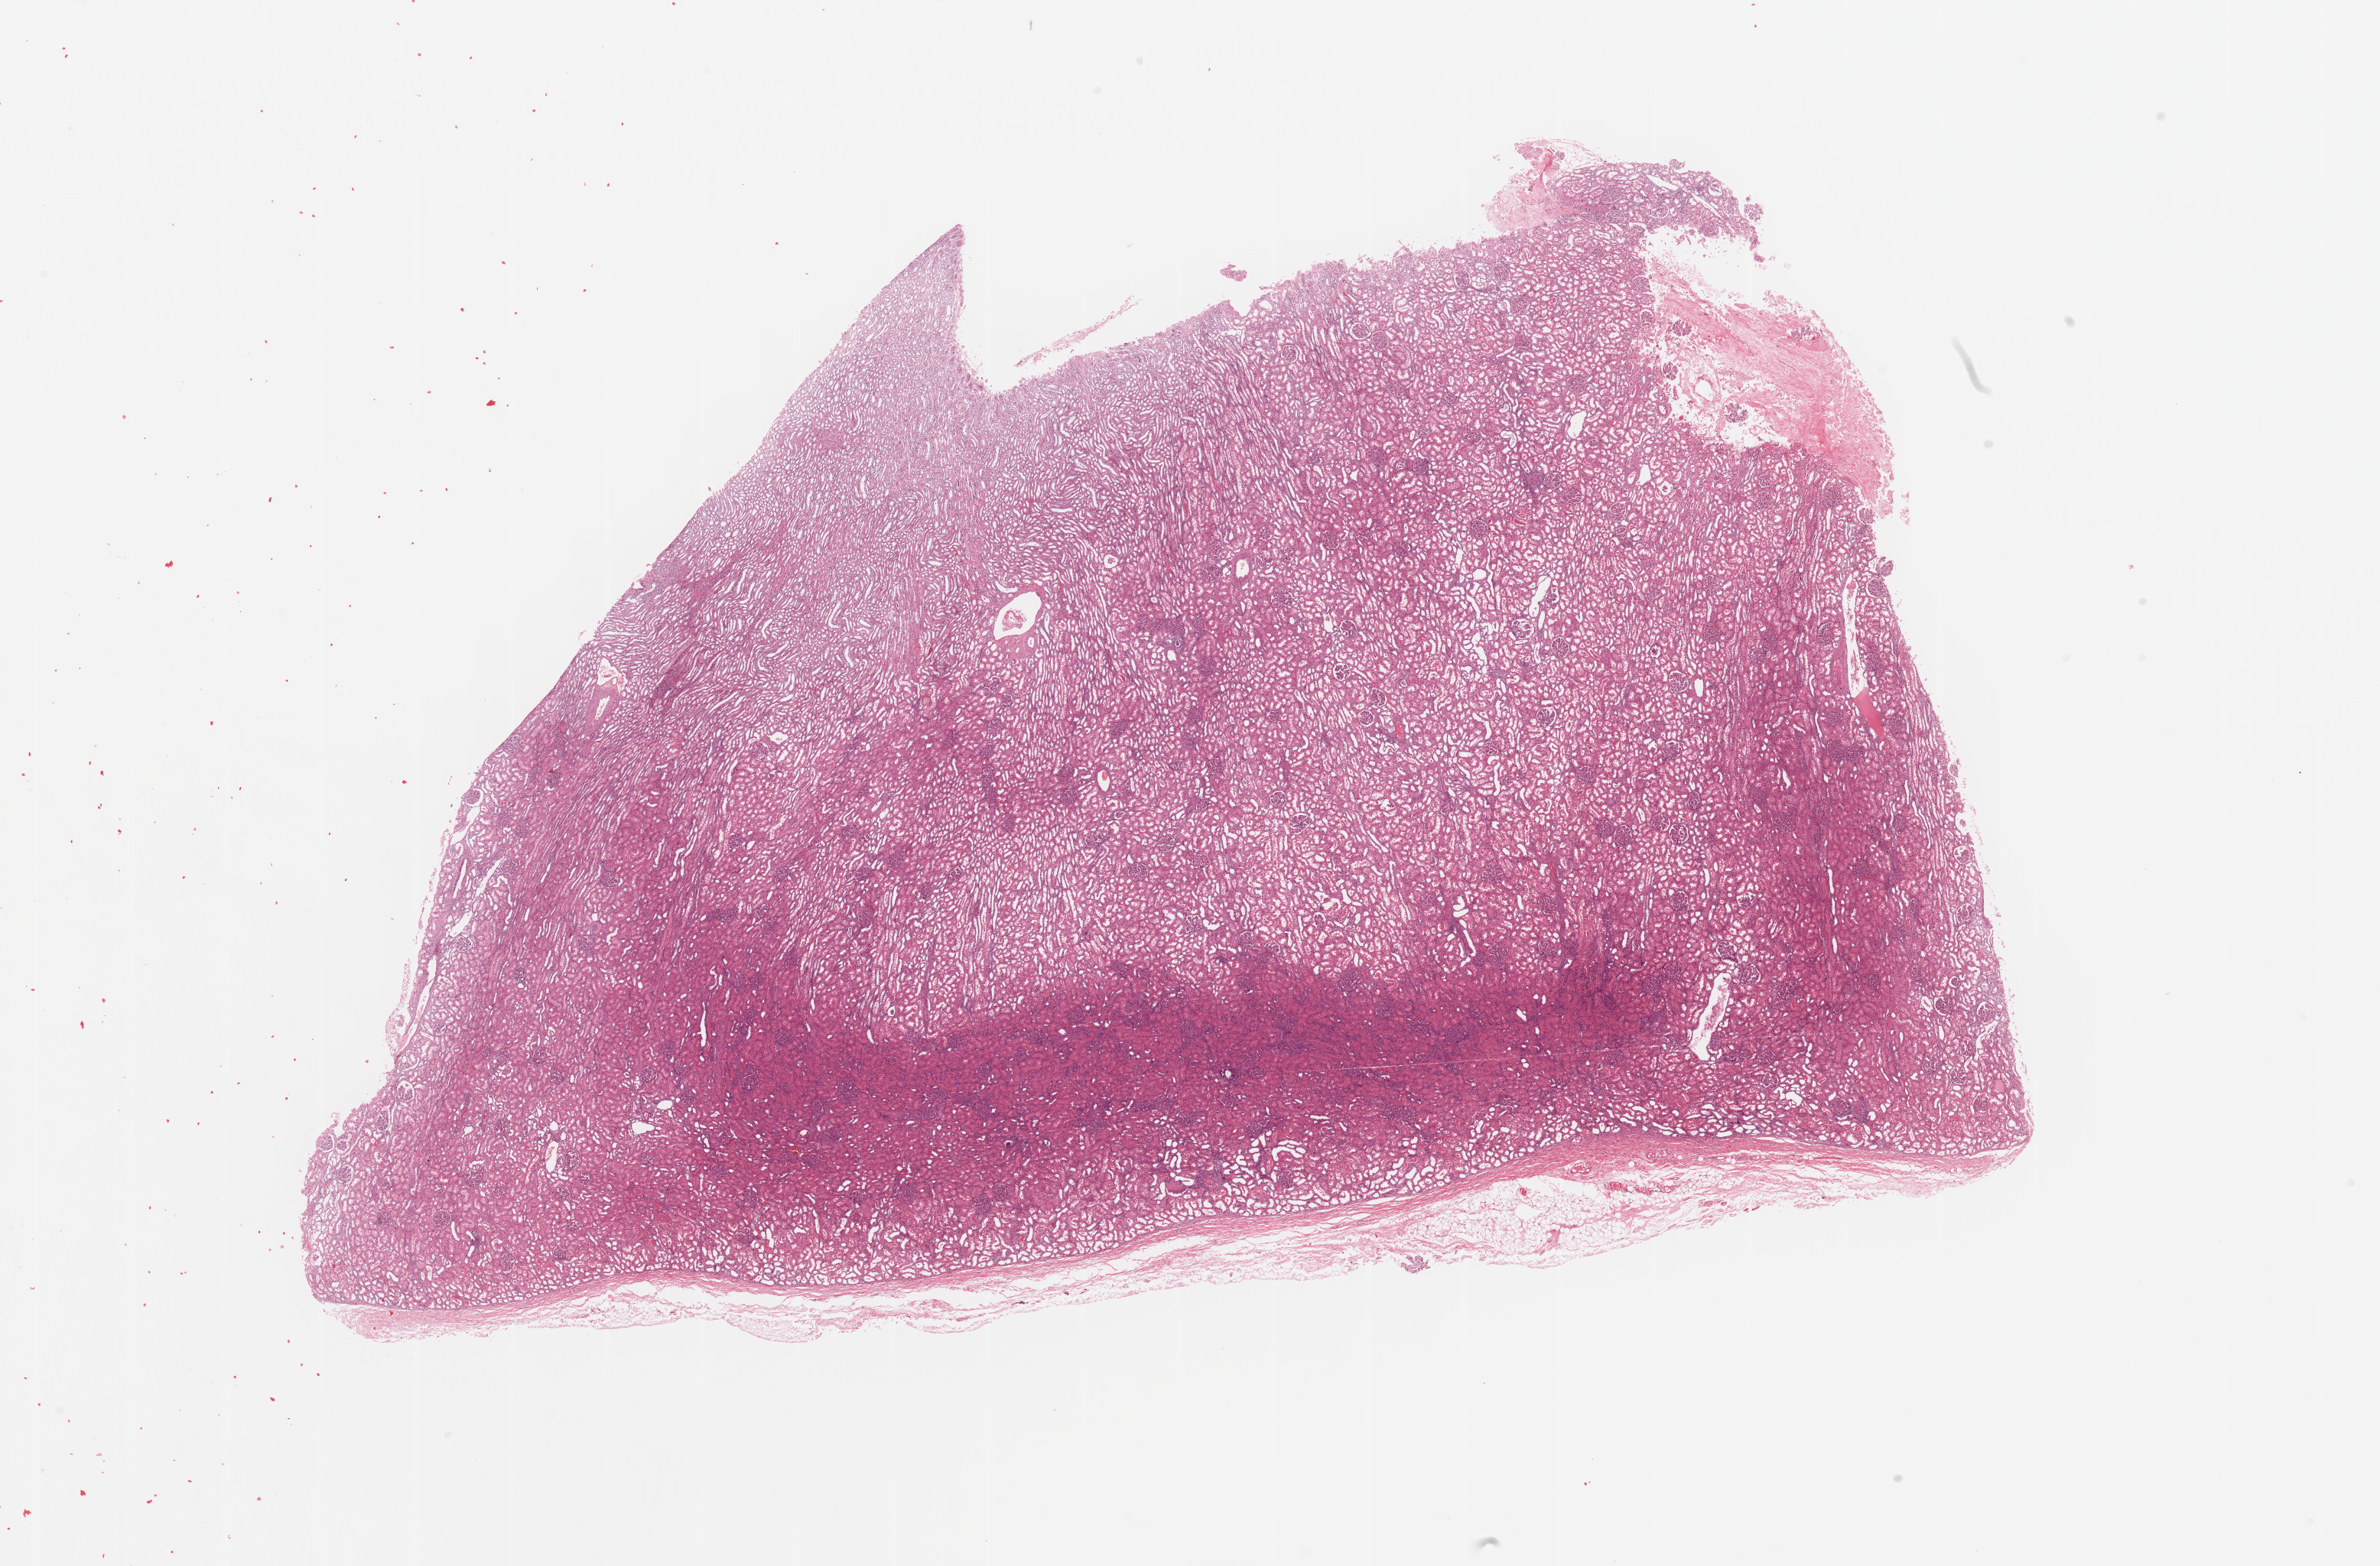
Digitized H&E-stained tissue section (whole slide) — low-resolution overview of the scanned area, about 24.6 x 16.2 mm (acquisition: 20x scan), kidney, normal (non-tumour) tissue. Patient: female, age 42 years.
• this section: normal (non-tumour) tissue from the same patient
• patient diagnosis: Renal cell carcinoma, NOS